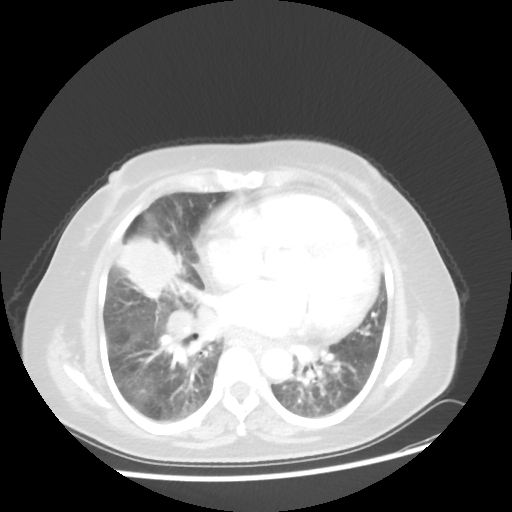
Chest CT, one axial slice. Slice 20 of 45 in the series (ordered by position). Lung window (W 1500 / L -600 HU). 5 mm slice thickness. 512 × 512 image matrix. Patient: female, 67 years. From the clinical record (not read from this slice): clinical TNM (as recorded): T2a N3 M1a.
Outlined on this slice (bounding box drawn by a radiologist):
- lung tumour (recorded histology: adenocarcinoma): bounding box (x1, y1, x2, y2) in pixels: (122, 231, 184, 299)